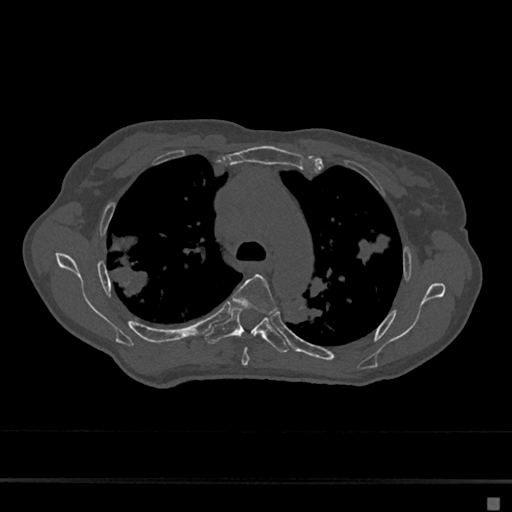
CT including the spine, one axial slice. Slice 480 of 797 in the series (ordered by position). Reconstruction kernel Br40s/3. 120 kVp. Bone window (W 1800 / L 400 HU). 512 × 512 image matrix. Female patient, age 68 years. Case-level facts recorded for this patient, not image findings: primary cancer: renal.
Annotated regions visible in this slice (semi-automatically segmented with operator editing):
- T4 vertebra: bounding box [x1, y1, x2, y2] px = [232, 274, 278, 366]
- T5 vertebra: [205, 307, 289, 353]